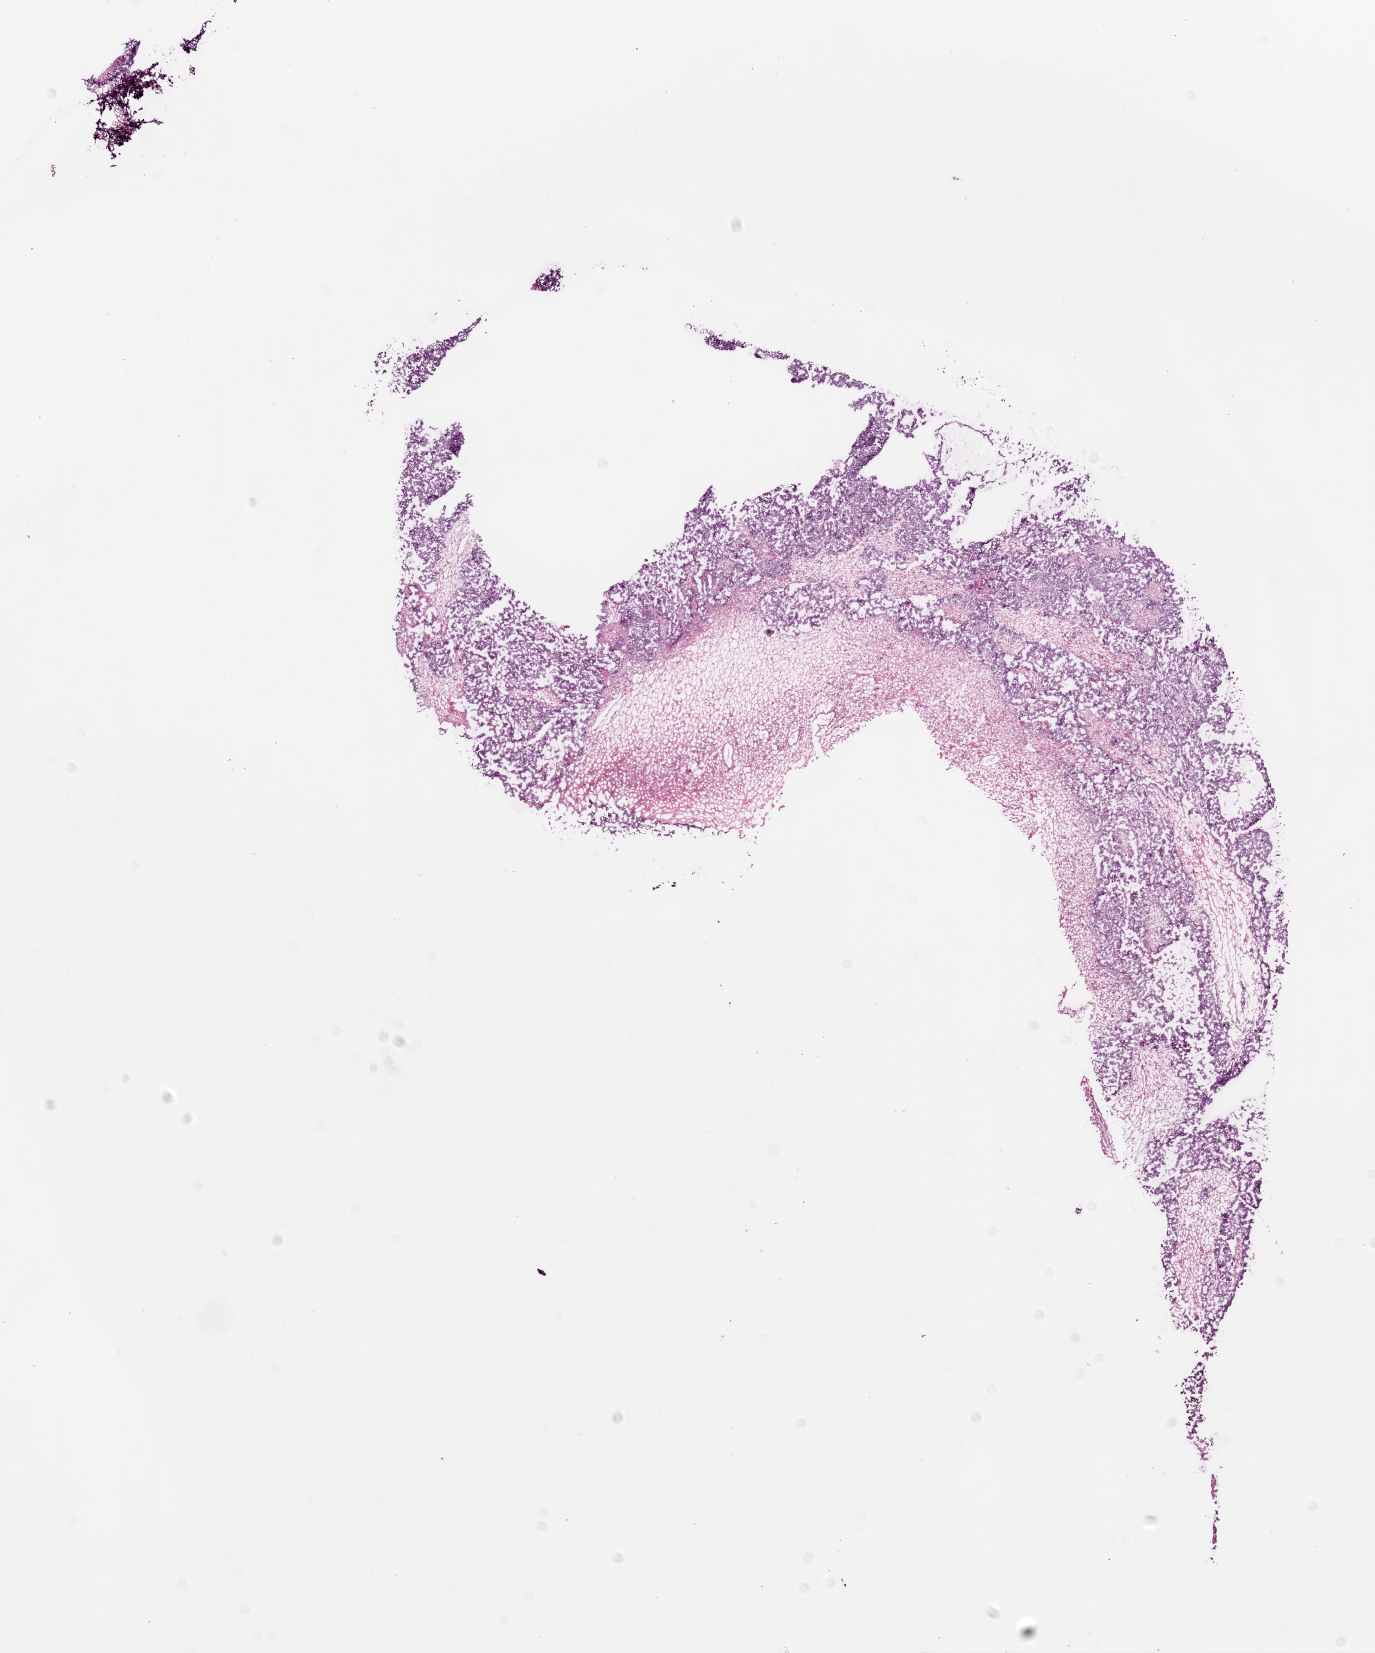
Hematoxylin and eosin (H&E) stained whole-slide image, whole scanned area (about 11.0 x 13.3 mm, slide scanned at 20x) shown as a low-resolution overview, frozen section, primary tumour sample from the ovary. Female patient; age at initial diagnosis 54 years. Histologic grade: G3 (poorly differentiated). Slide review estimates, as recorded: tumour cells 55%, tumour nuclei 70%, normal cells 0%, stromal cells 40%, necrosis 5%.
FIGO stage: IIIA. Histologic diagnosis: Serous cystadenocarcinoma, NOS. Laterality: right.